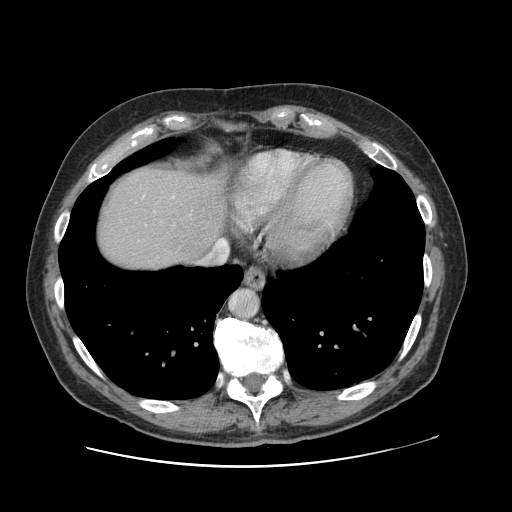
Contrast-enhanced abdominal CT, one axial slice; slice 108 of 138 in the series (ordered by position); 120 kVp; soft-tissue window (W 400 / L 40 HU); 512 × 512 image matrix. Male patient, age 71 years. From the clinical record (not read from this slice): diagnosis: colorectal cancer liver metastases, imaged before liver resection; multiple liver metastases: no; largest metastasis: 3.3 cm; disease in both lobes: no.
Outlined on this slice (expert manual segmentation):
- hepatic veins: bounding box [x1, y1, x2, y2] px = [198, 239, 229, 266]
- liver: [95, 166, 228, 273]
- planned liver remnant (the part of the liver to remain after resection): [96, 167, 219, 272]